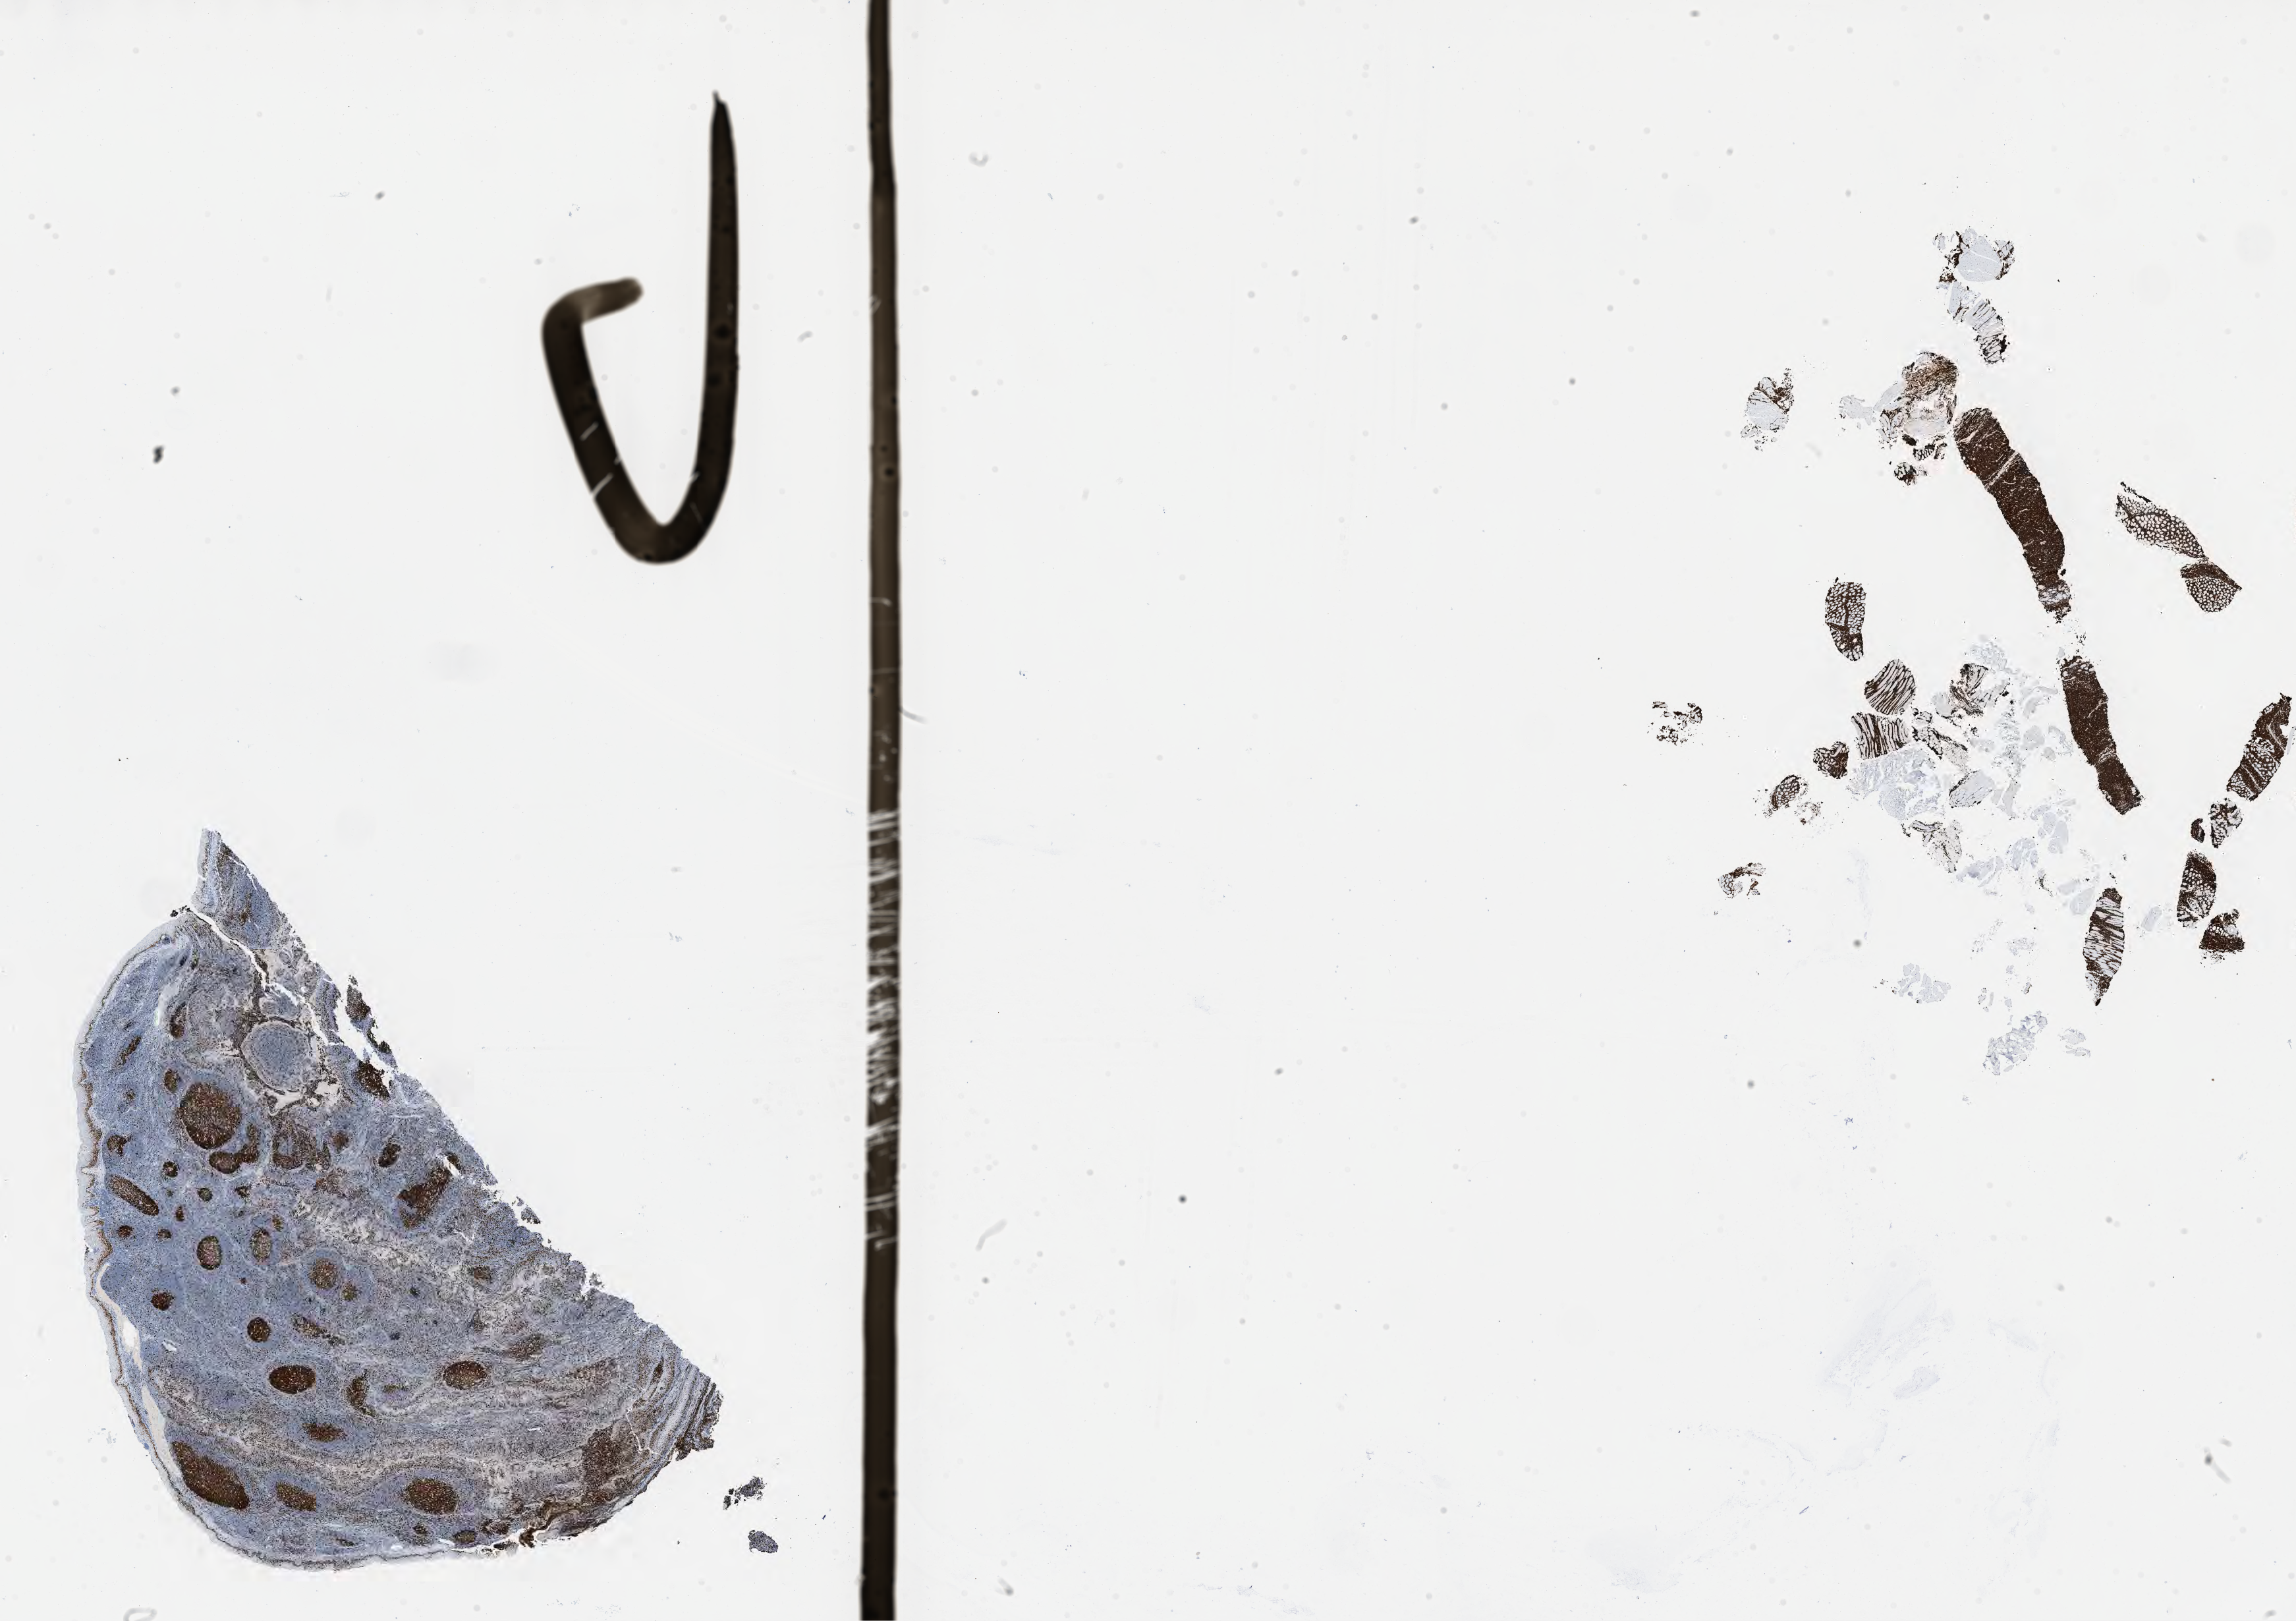
IHC for Ki-67, whole-slide image — whole scanned area (about 28.2 x 19.9 mm) shown as a low-resolution overview. Specimen: tumor tissue. Anatomic site: retroperitoneum. Patient female; 53 years old.
Histologic diagnosis: Burkitt lymphoma, NOS.